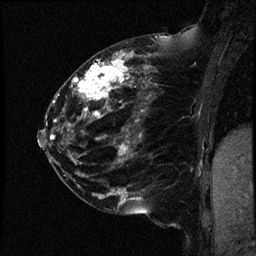
Breast MRI (dynamic contrast-enhanced), one sagittal slice; position 23 of 44 along the scan axis; dynamic contrast-enhanced study with each time point stored as its own series, time point 2 of 4 at this slice position (early post-contrast, ordered by acquisition time); 1.5 T; TE 4.2 ms, TR 17.7 ms; 2 mm slice thickness; 256 × 256 image matrix, field of view 200 × 200 mm. Female patient, age 52 years. From the clinical record (not read from this slice): setting: breast cancer imaged before/during neoadjuvant chemotherapy; receptor status: HR-positive, HER2-negative.
Annotated regions visible in this slice (semi-automatic segmentation, software-assisted and operator-edited):
- analysis volume of interest (the breast-tissue region the enhancement analysis was run in; not a lesion): bounding box (x1, y1, x2, y2) in pixels: (47, 48, 163, 147)
- tumour enhancement mask (voxels above the 100 % enhancement threshold inside the analysis volume of interest): (51, 52, 149, 147)